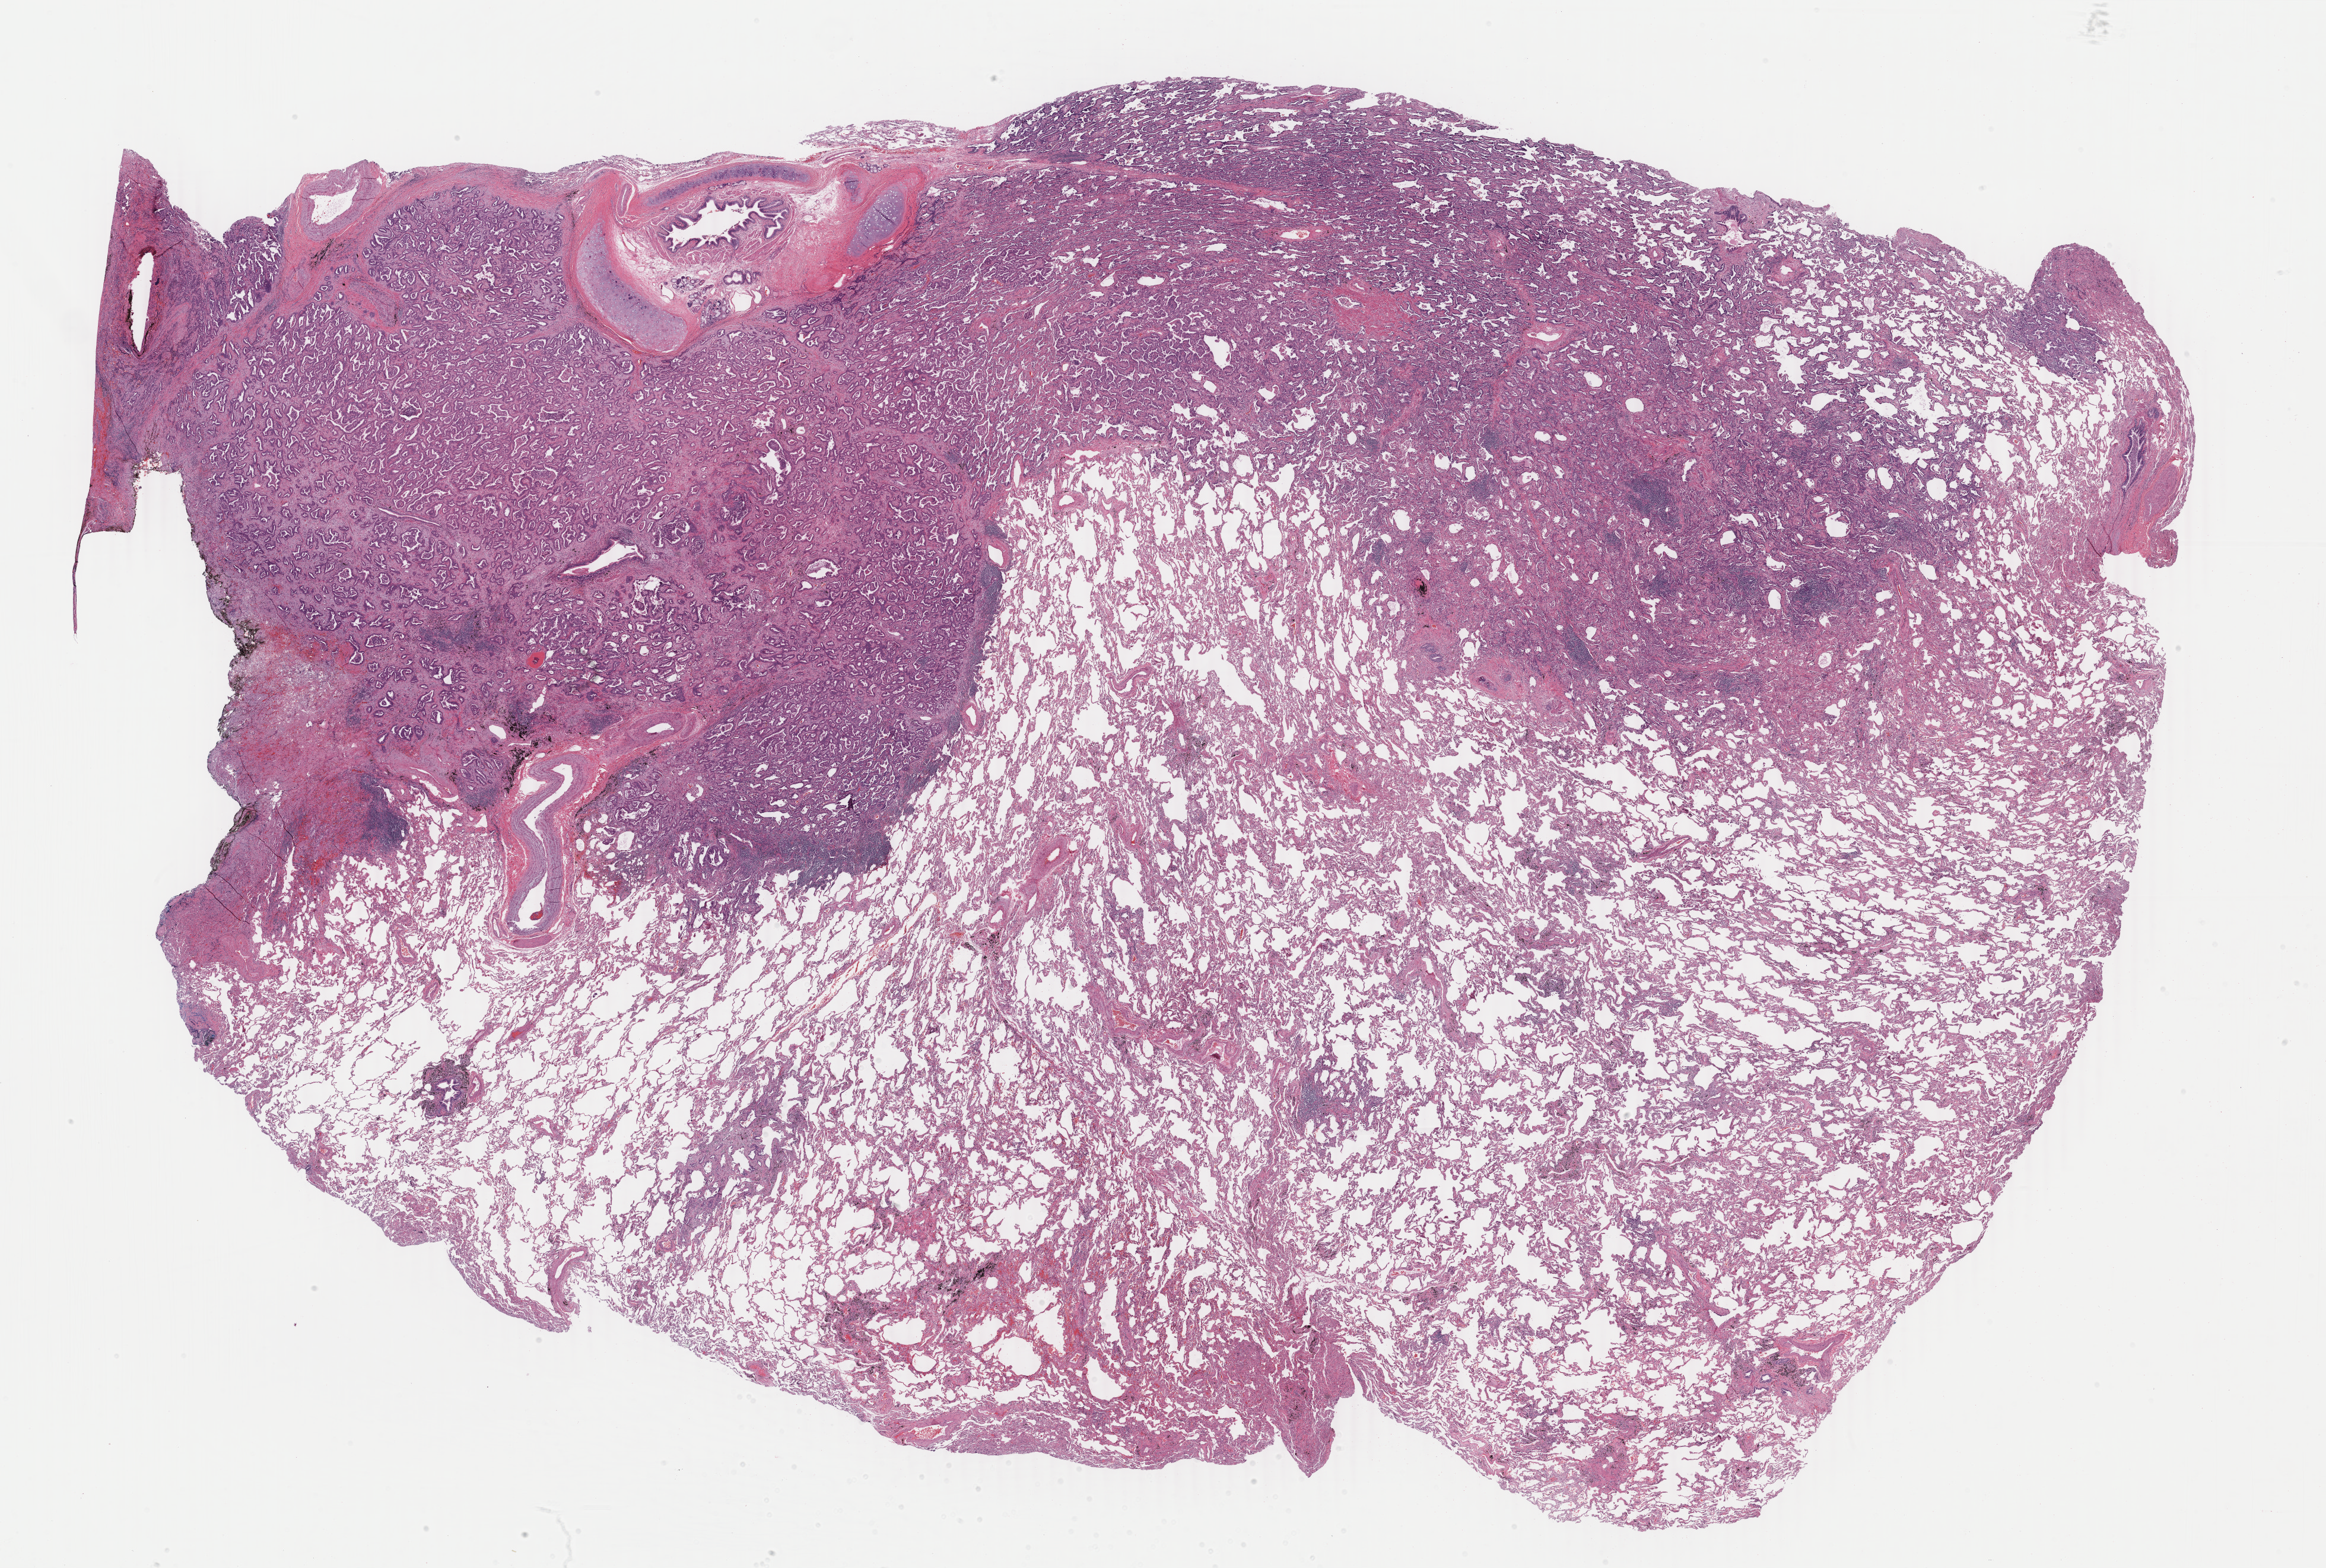
H&E whole-slide image, low-resolution overview of the scanned area, about 31.2 x 21.0 mm; formalin-fixed paraffin-embedded (FFPE) diagnostic section; sample: primary tumour, lung. Female, age 69 years at initial diagnosis.
AJCC pathologic stage: IA (7th edition). Diagnosis: Adenocarcinoma with mixed subtypes (upper lobe, lung).